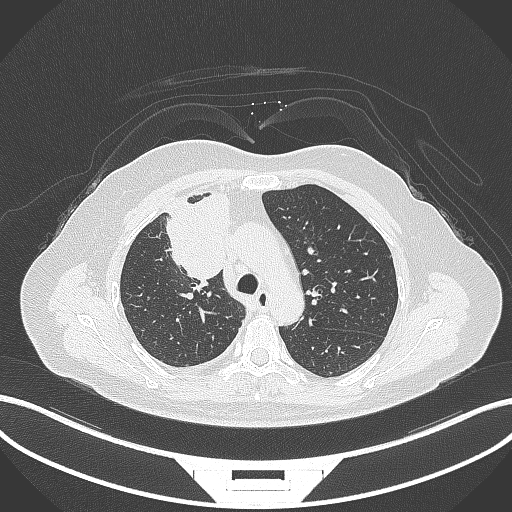
Chest CT, one axial slice; slice 204 of 305 in the series (ordered by position); lung window (W 1500 / L -600 HU); 512 × 512 image matrix. Patient: female, 52 years. From the clinical record (not read from this slice): clinical TNM (as recorded): T3 N1 M1.
Annotated regions visible in this slice (rectangle marked by the reading radiologist):
- lung tumour (recorded histology: adenocarcinoma): bounding box <161,194,237,282> (left, top, right, bottom; pixels)